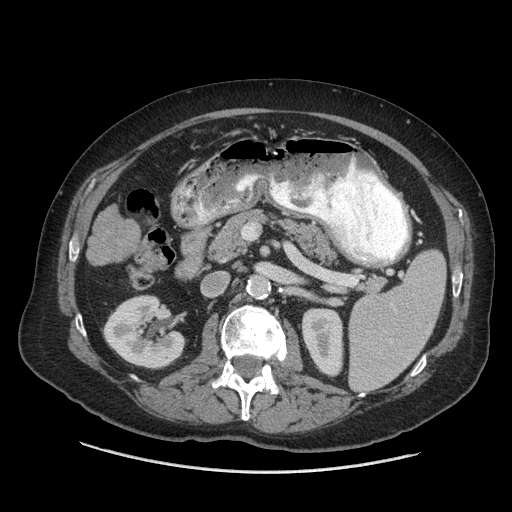
Contrast-enhanced abdominal CT (liver protocol), one axial slice. Position 20 of 77 along the scan axis. Reconstruction kernel STANDARD. Soft-tissue window (W 400 / L 40 HU). 2.5 mm slice thickness. 512 × 512 image matrix, field of view 420 × 420 mm. From the clinical record (not read from this slice): diagnosis: hepatocellular carcinoma (patient treated with transarterial chemoembolisation; whether this scan precedes or follows treatment is not stated here); TNM stage (as recorded): Stage-I; Child-Pugh class: A; tumour differentiation: well differentiated; tumour nodularity: uninodular.
Outlined on this slice (semi-automatic segmentation, software-assisted and operator-edited):
- liver parenchyma outside the tumour (the mass and vessels are separate outlines, so this box may not span the whole liver): bounding box <95,206,120,230> (left, top, right, bottom; pixels)